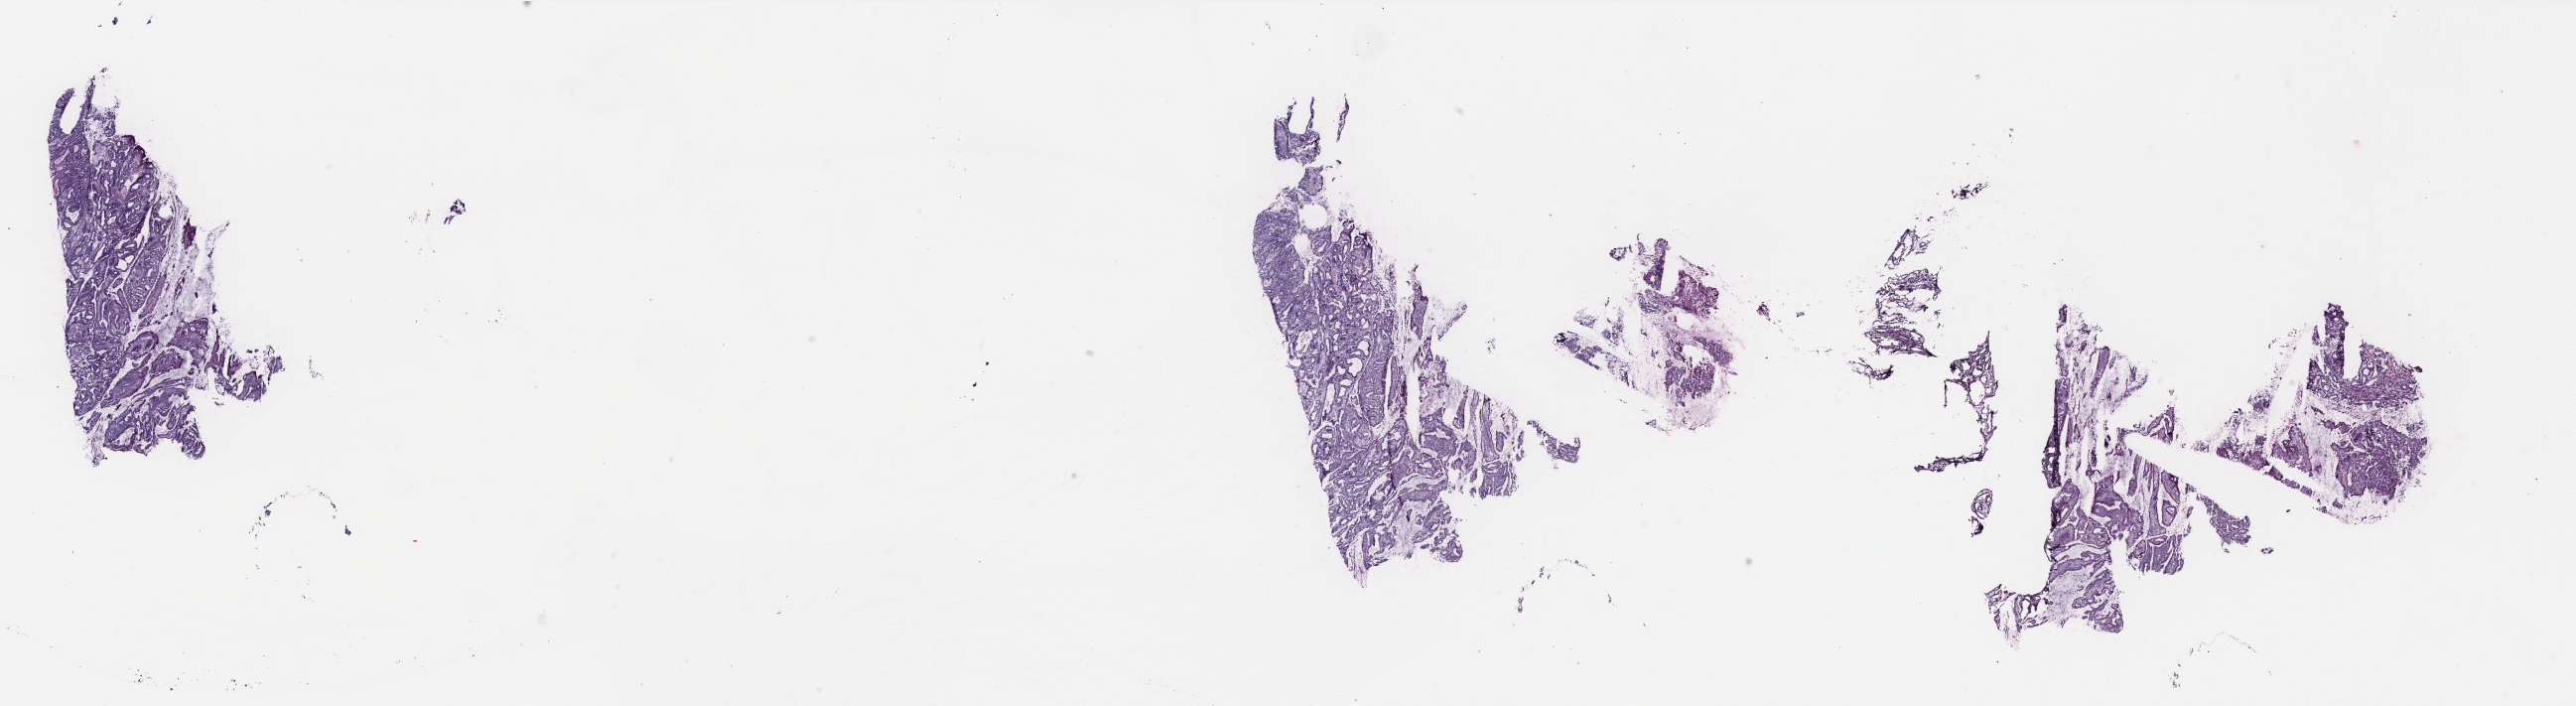
Digitized H&E tissue section (whole slide), whole scanned area (about 41.6 x 11.4 mm, acquisition: 40x scan) shown as a low-resolution overview, frozen section from the bottom of the tissue portion, primary tumour sample from the uterus. Female patient; age at initial diagnosis 60 years. Histologic grade: G2 (moderately differentiated). Pathologist review of this section (percent, as recorded): tumour cells 100%, tumour nuclei 75%, normal cells 0%, stromal cells 0%, necrosis 0%. Inflammatory infiltration, as recorded: lymphocyte infiltration 0%, monocyte infiltration 0%, neutrophil infiltration 0%.
FIGO stage: IIIC1. Pathologic diagnosis: Endometrioid adenocarcinoma, NOS (endometrium).